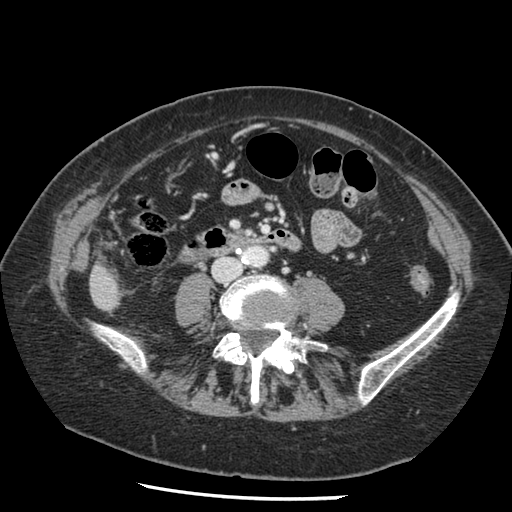
Contrast-enhanced abdominal CT, one axial slice; slice 15 of 148 in the series (ordered by position); 120 kVp; intravenous contrast given; soft-tissue window (W 400 / L 40 HU); 512 × 512 image matrix, field of view 330 × 330 mm. Female patient, age 85 years. Case-level facts recorded for this patient, not image findings: diagnosis: colorectal cancer liver metastases, imaged before liver resection; multiple liver metastases: no; largest metastasis: 0.9 cm; chemotherapy before resection: yes.
Annotated regions visible in this slice (outlined manually by an expert reader):
- liver: bounding box [x1, y1, x2, y2] px = [91, 267, 120, 310]
- planned liver remnant (the part of the liver to remain after resection): [91, 267, 120, 310]